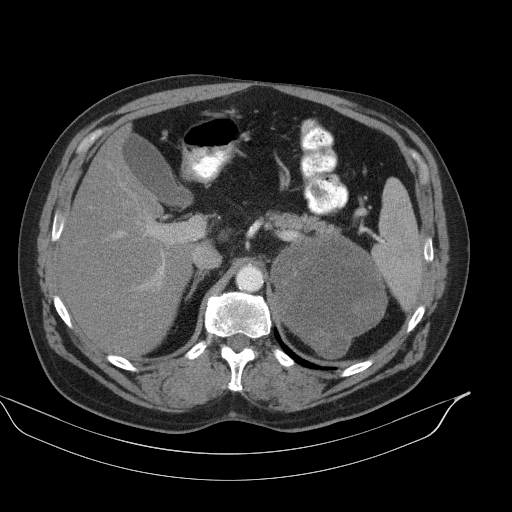
Contrast-enhanced abdominal CT, one axial slice. Position 70 of 92 along the scan axis. Reconstruction kernel B41s. Intravenous contrast given. Soft-tissue window (W 400 / L 40 HU). 5 mm slice thickness. 512 × 512 image matrix. Patient: male, 56 years. Case-level facts recorded for this patient, not image findings: diagnosis: adrenocortical carcinoma; tumour side: left adrenal.
Structures marked on this image (semi-automatically segmented with operator editing):
- mass: bounding box [x1, y1, x2, y2] px = [272, 237, 385, 357]